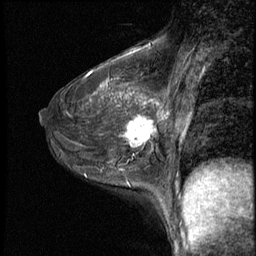
Breast MRI (dynamic contrast-enhanced), one sagittal slice. Slice 33 of 50 in the series (ordered by position). 3 images stored at this slice position (order not interpretable as contrast timing). 1.5 T. TE 4.2 ms, TR 8.7 ms. 256 × 256 image matrix, field of view 180 × 180 mm. Patient: female, 43 years. Case-level facts recorded for this patient, not image findings: setting: breast cancer imaged before/during neoadjuvant chemotherapy; receptor status: HR-positive, HER2-negative.
Structures marked on this image (semi-automatically segmented with operator editing):
- analysis volume of interest (the breast-tissue region the enhancement analysis was run in; not a lesion): bounding box (x1, y1, x2, y2) in pixels: (122, 109, 159, 155)
- tumour enhancement mask (voxels above the 140 % enhancement threshold inside the analysis volume of interest): (126, 117, 157, 147)